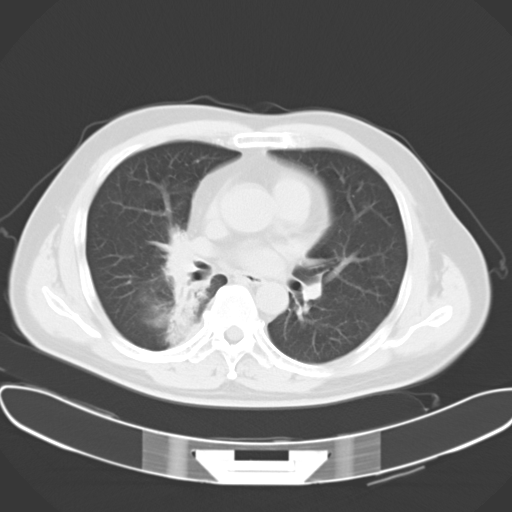
Chest CT, one axial slice. Slice 15 of 28 in the series (ordered by position). Reconstruction kernel B40f. 120 kVp. Lung window (W 1500 / L -600 HU). 10 mm slice thickness. 512 × 512 image matrix, field of view 388 × 388 mm. Patient: male, 48 years. From the clinical record (not read from this slice): clinical TNM (as recorded): T1a N1 M1c; histopathological grade: G3.
Annotated regions visible in this slice (bounding box drawn by a radiologist):
- lung tumour (recorded histology: adenocarcinoma): bounding box [x1, y1, x2, y2] px = [163, 226, 215, 307]